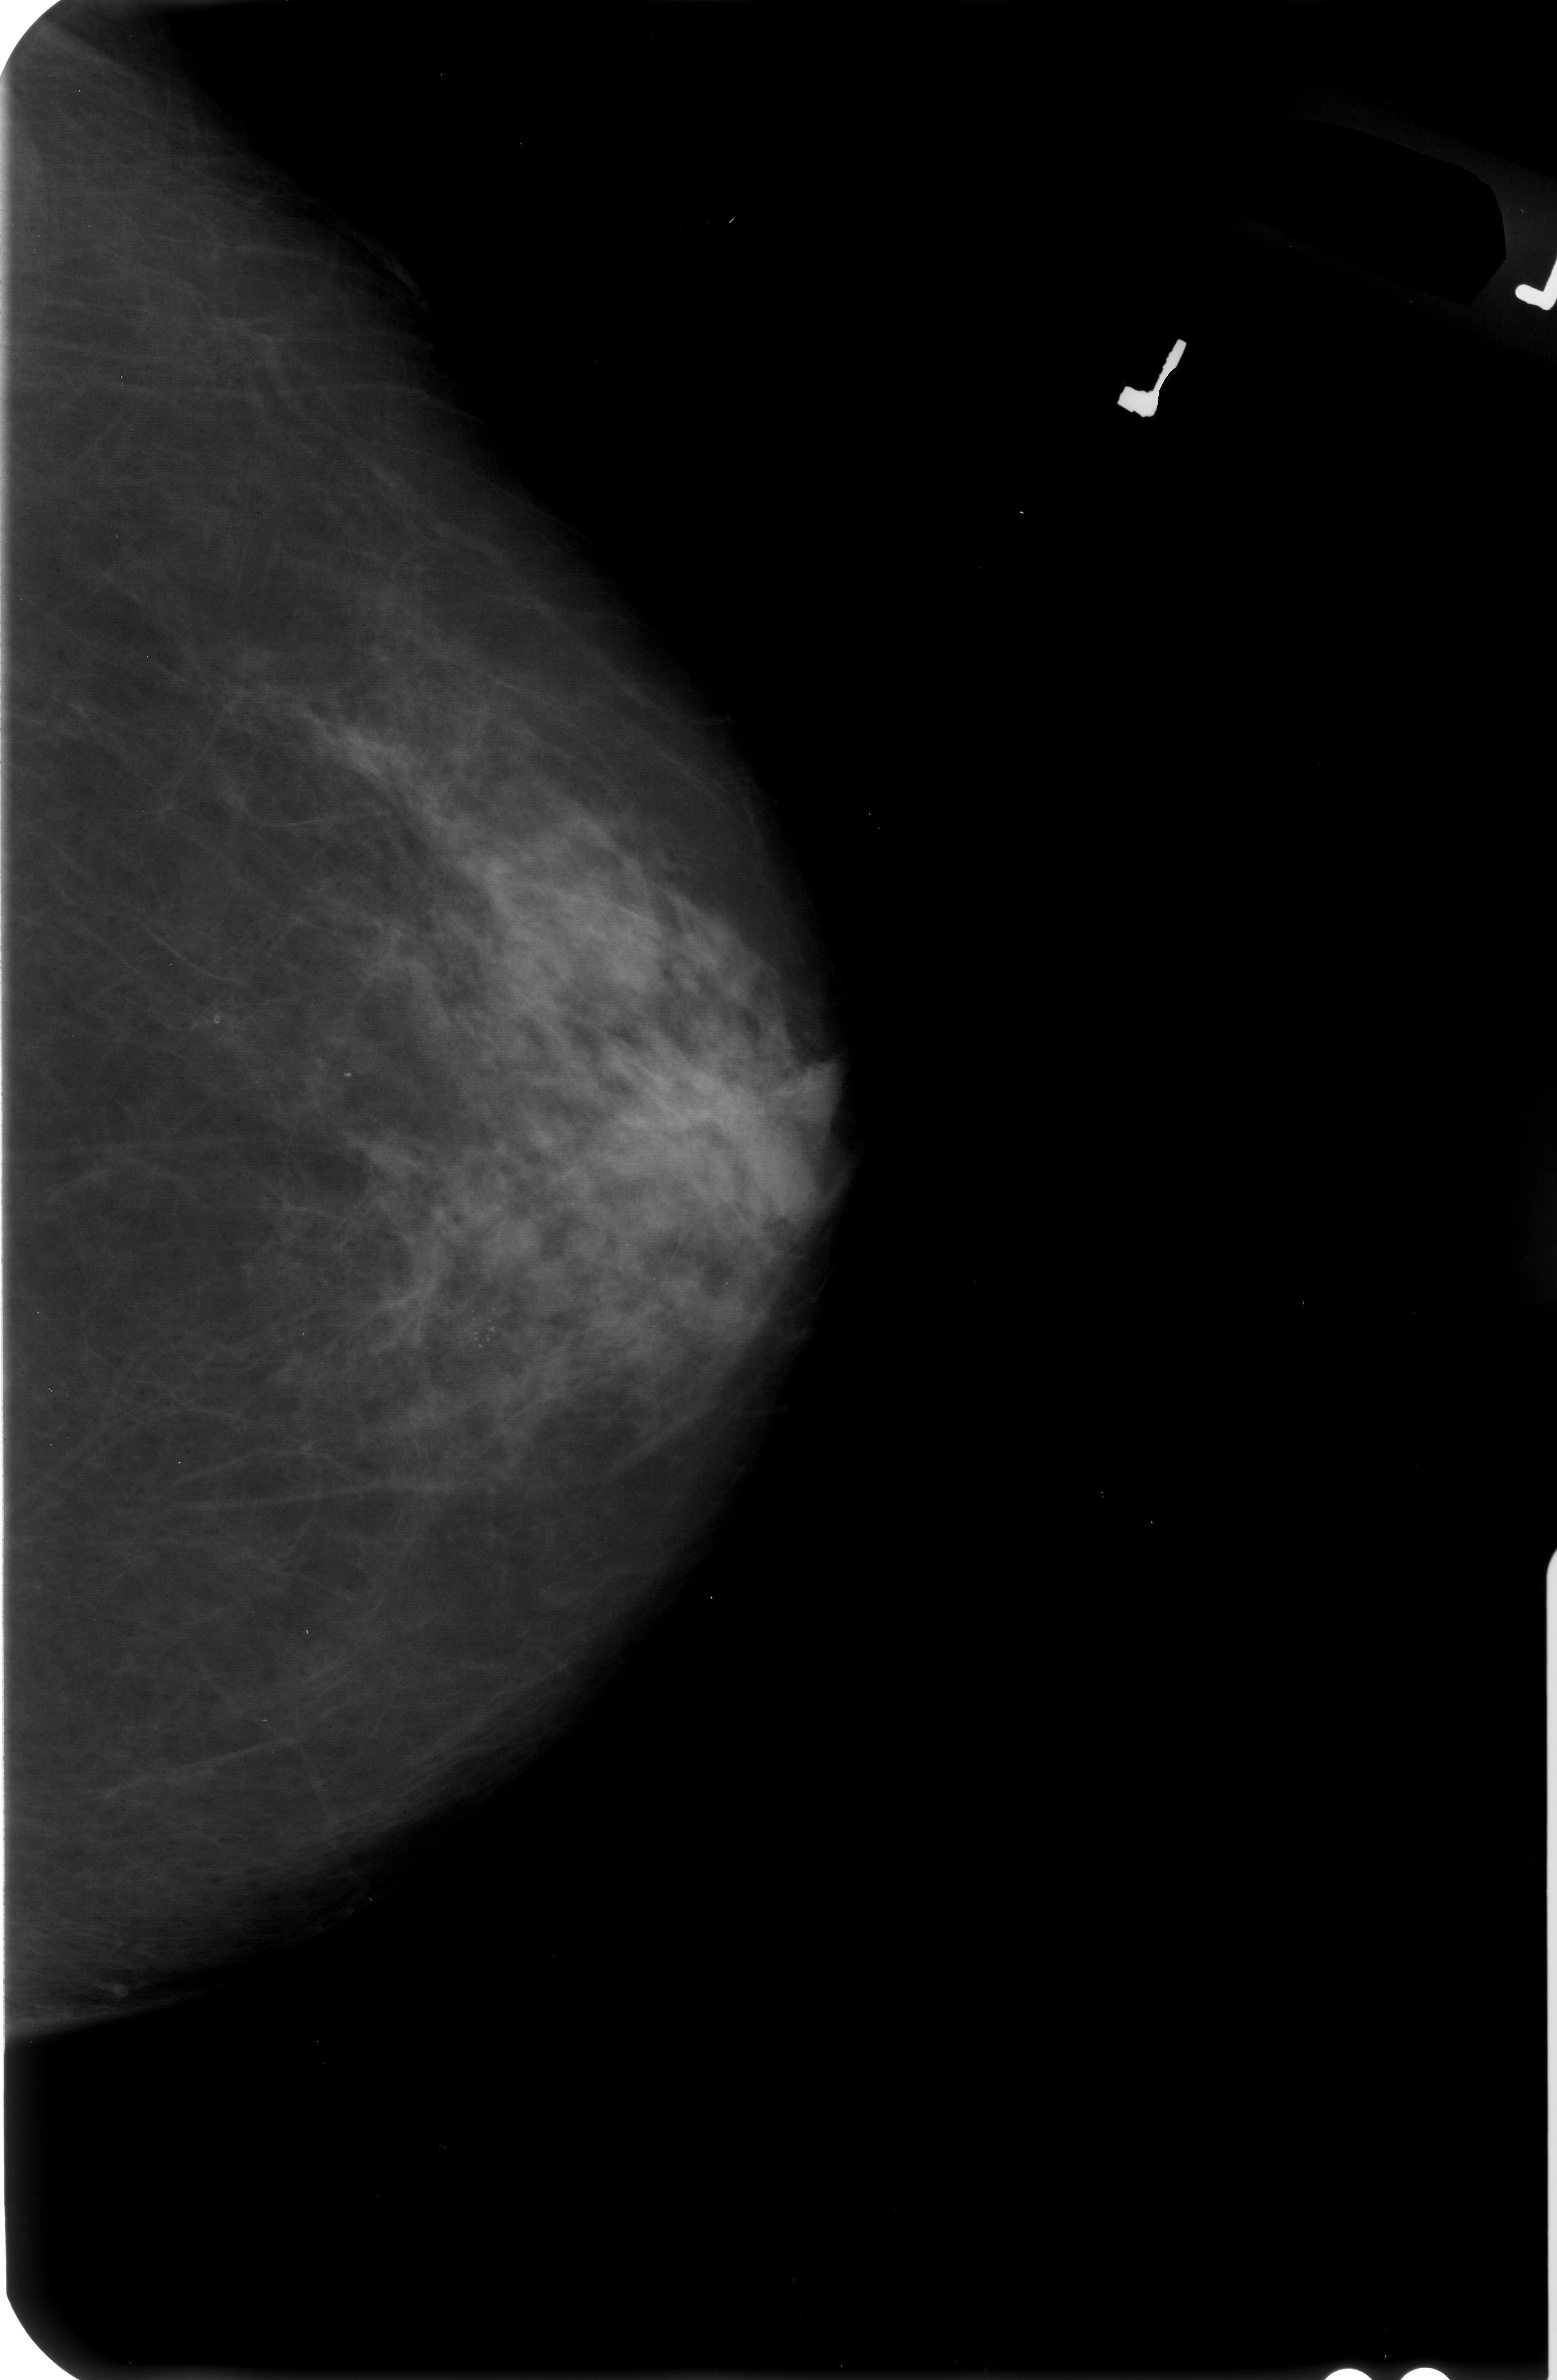
Digitized screen-film mammogram, left breast, craniocaudal (CC) view, breast composition: scattered fibroglandular densities (BI-RADS density category 2 of 4).
Radiologist-marked abnormalities on this image: calcifications, morphology punctate / pleomorphic, distribution clustered; BI-RADS assessment category 4; subtlety rating 3 on a 1 (subtle) to 5 (obvious) scale; pathology (as recorded): malignant.